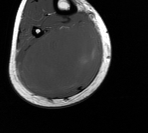
MRI of an extremity soft-tissue mass, one axial slice. Slice 53 of 76 in the series (ordered by position). MR volume resampled by the dataset authors to the PET/CT grid (not the native acquisition matrix). 3.27 mm slice thickness. 148 × 133 image matrix, field of view 145 × 130 mm. Male patient. From the clinical record (not read from this slice): histological type: liposarcoma - round cell; grade: high; site of the primary tumour: right calf.
Outlined on this slice (expert contour drawn on MRI and transferred to this co-registered scan by the dataset authors):
- gross tumour volume (mass): box from (x=17, y=21) to (x=100, y=95) px